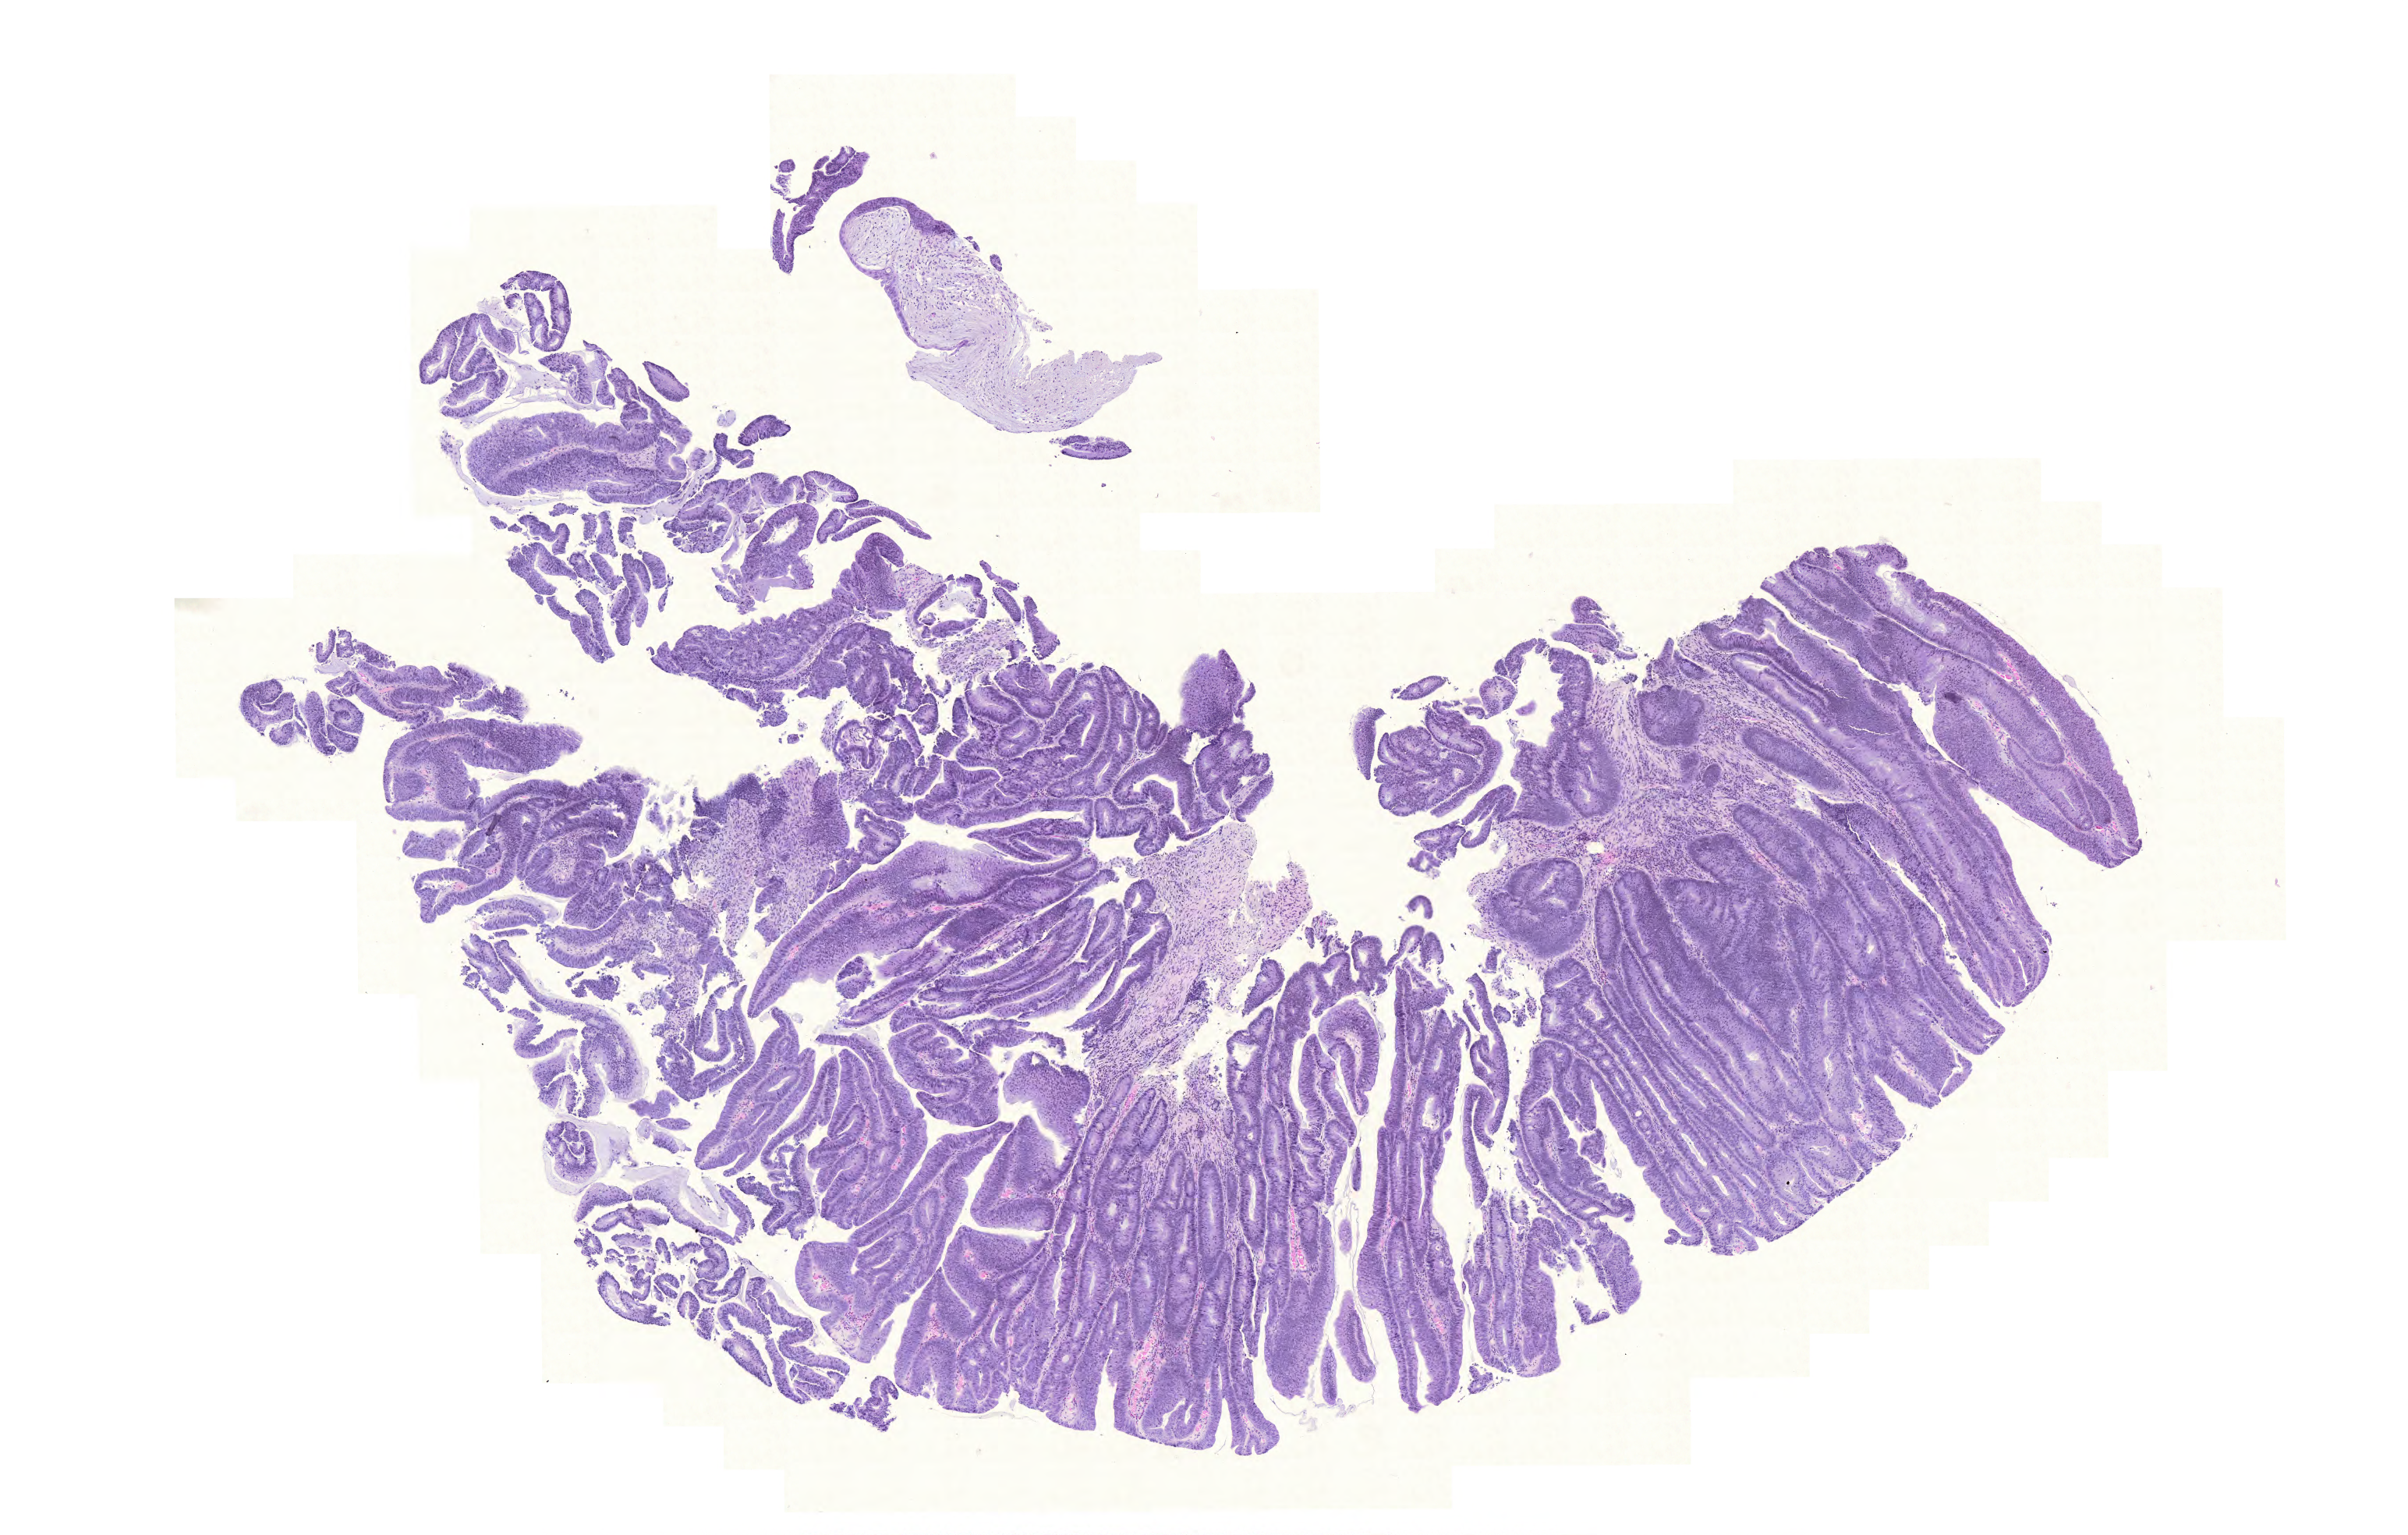
H&E-stained whole-slide image — low-resolution overview of the scanned area, about 11.5 x 7.3 mm (slide scanned at 20x). FFPE section. Sample: primary tumour, colon. Male, age 88 years at initial diagnosis.
AJCC pathologic stage: IIA. Histologic diagnosis: Mucinous adenocarcinoma.